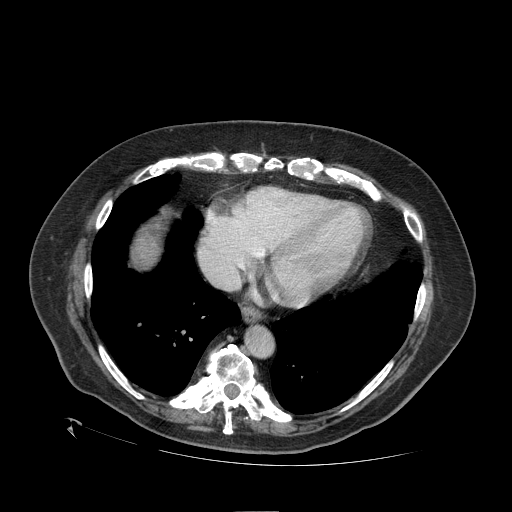
Contrast-enhanced abdominal CT (liver protocol), one axial slice. Position 100 of 109 along the scan axis. Reconstruction kernel STANDARD. One of 2 acquisitions stored at this slice position. Soft-tissue window (W 400 / L 40 HU). 512 × 512 image matrix. From the clinical record (not read from this slice): diagnosis: hepatocellular carcinoma (patient treated with transarterial chemoembolisation; whether this scan precedes or follows treatment is not stated here); TNM stage (as recorded): Stage-I; Child-Pugh class: A; tumour size: 4.6 cm.
Outlined on this slice (semi-automatically segmented with operator editing):
- liver parenchyma outside the tumour (the mass and vessels are separate outlines, so this box may not span the whole liver): bounding box <132,220,163,268> (left, top, right, bottom; pixels)